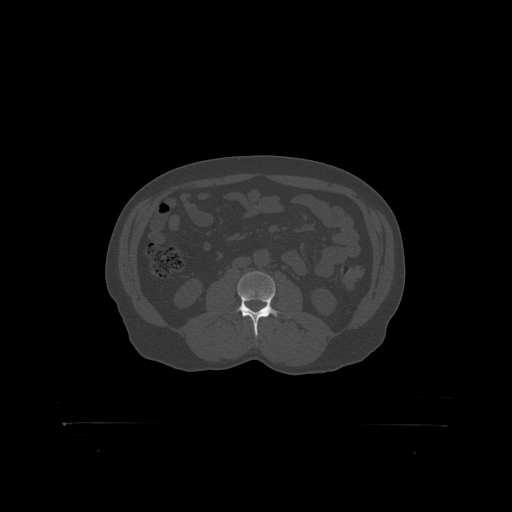
CT including the spine, one axial slice; slice 265 of 399 in the series (ordered by position); reconstruction kernel STANDARD; 120 kVp; bone window (W 1800 / L 400 HU); 1.25 mm slice thickness; 512 × 512 image matrix, field of view 650 × 650 mm. Male patient, age 46 years. From the clinical record (not read from this slice): primary cancer: skin.
Annotated regions visible in this slice (semi-automatically segmented with operator editing):
- L3 vertebra: bounding box <237,272,280,319> (left, top, right, bottom; pixels)